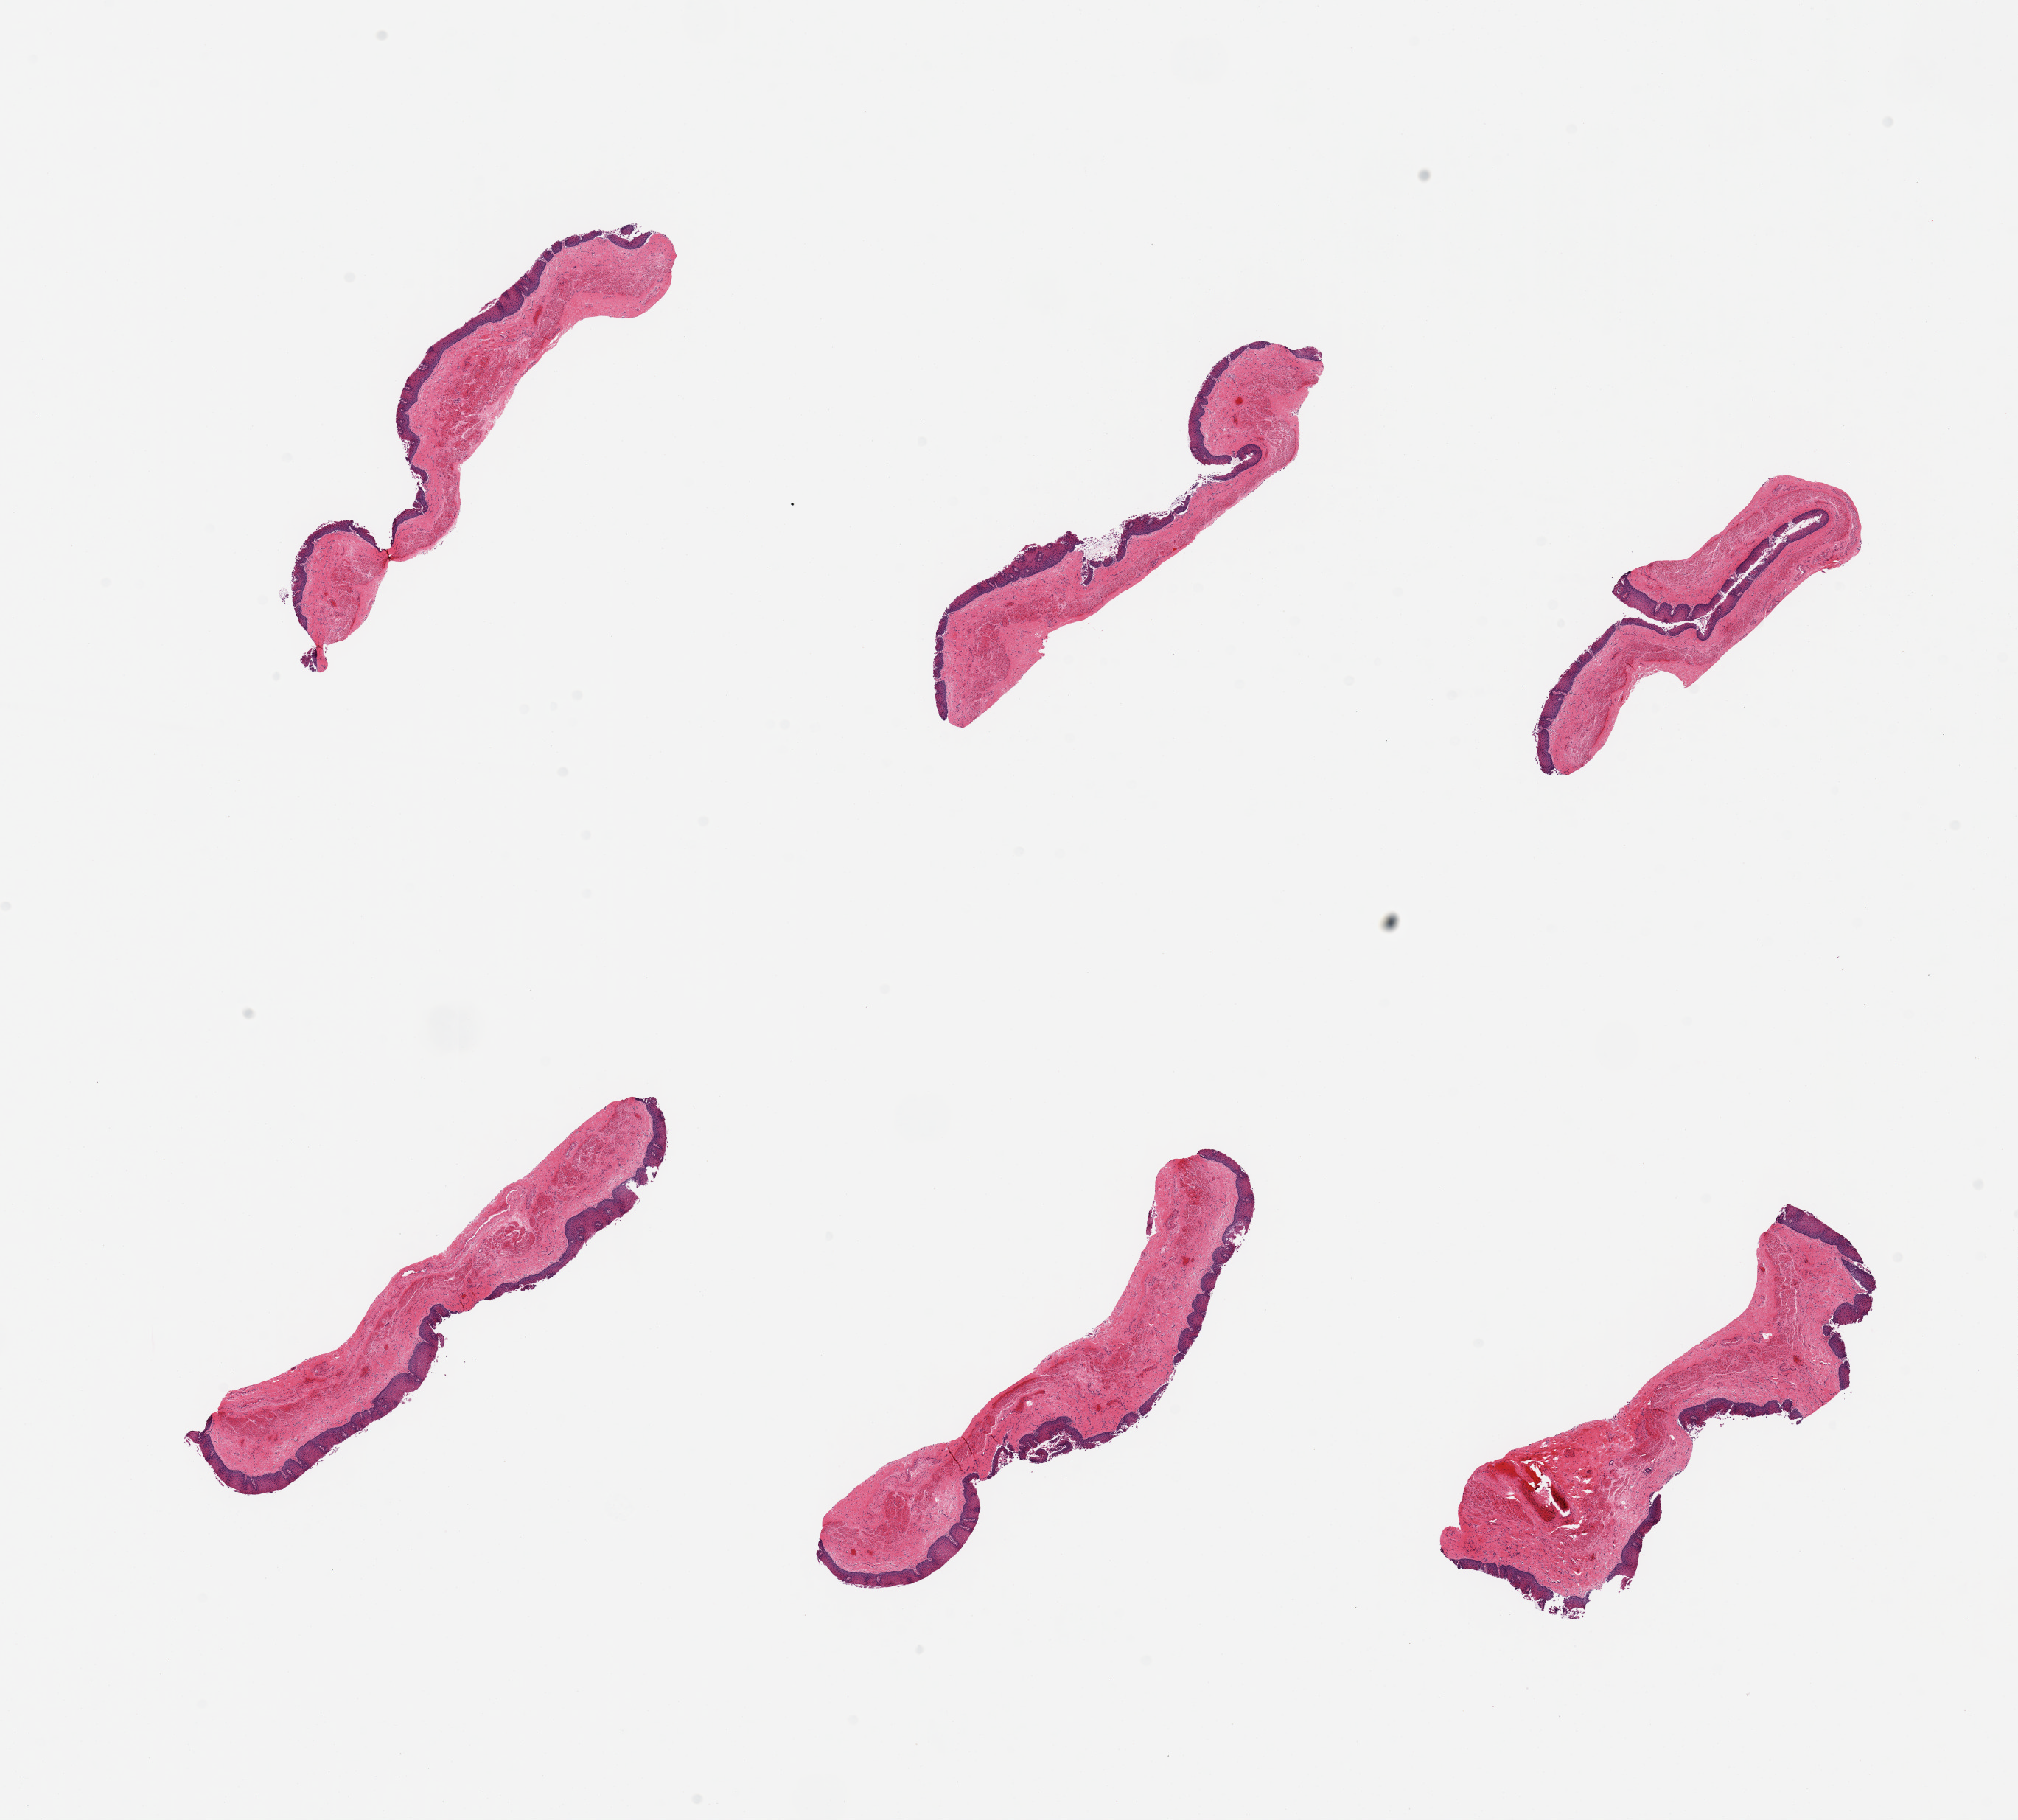
H&E whole-slide image, shown as a low-resolution overview of the whole scanned area (about 21.7 x 19.5 mm, from a 20x scan). PAXgene-fixed paraffin-embedded (PFPE) section. Sampled site (target tissue): esophageal mucous membrane. Donor tissue sample.
Reviewer comment on this tissue sample: 6 pieces; focal sloughing of epithelium; vegetable remnants.